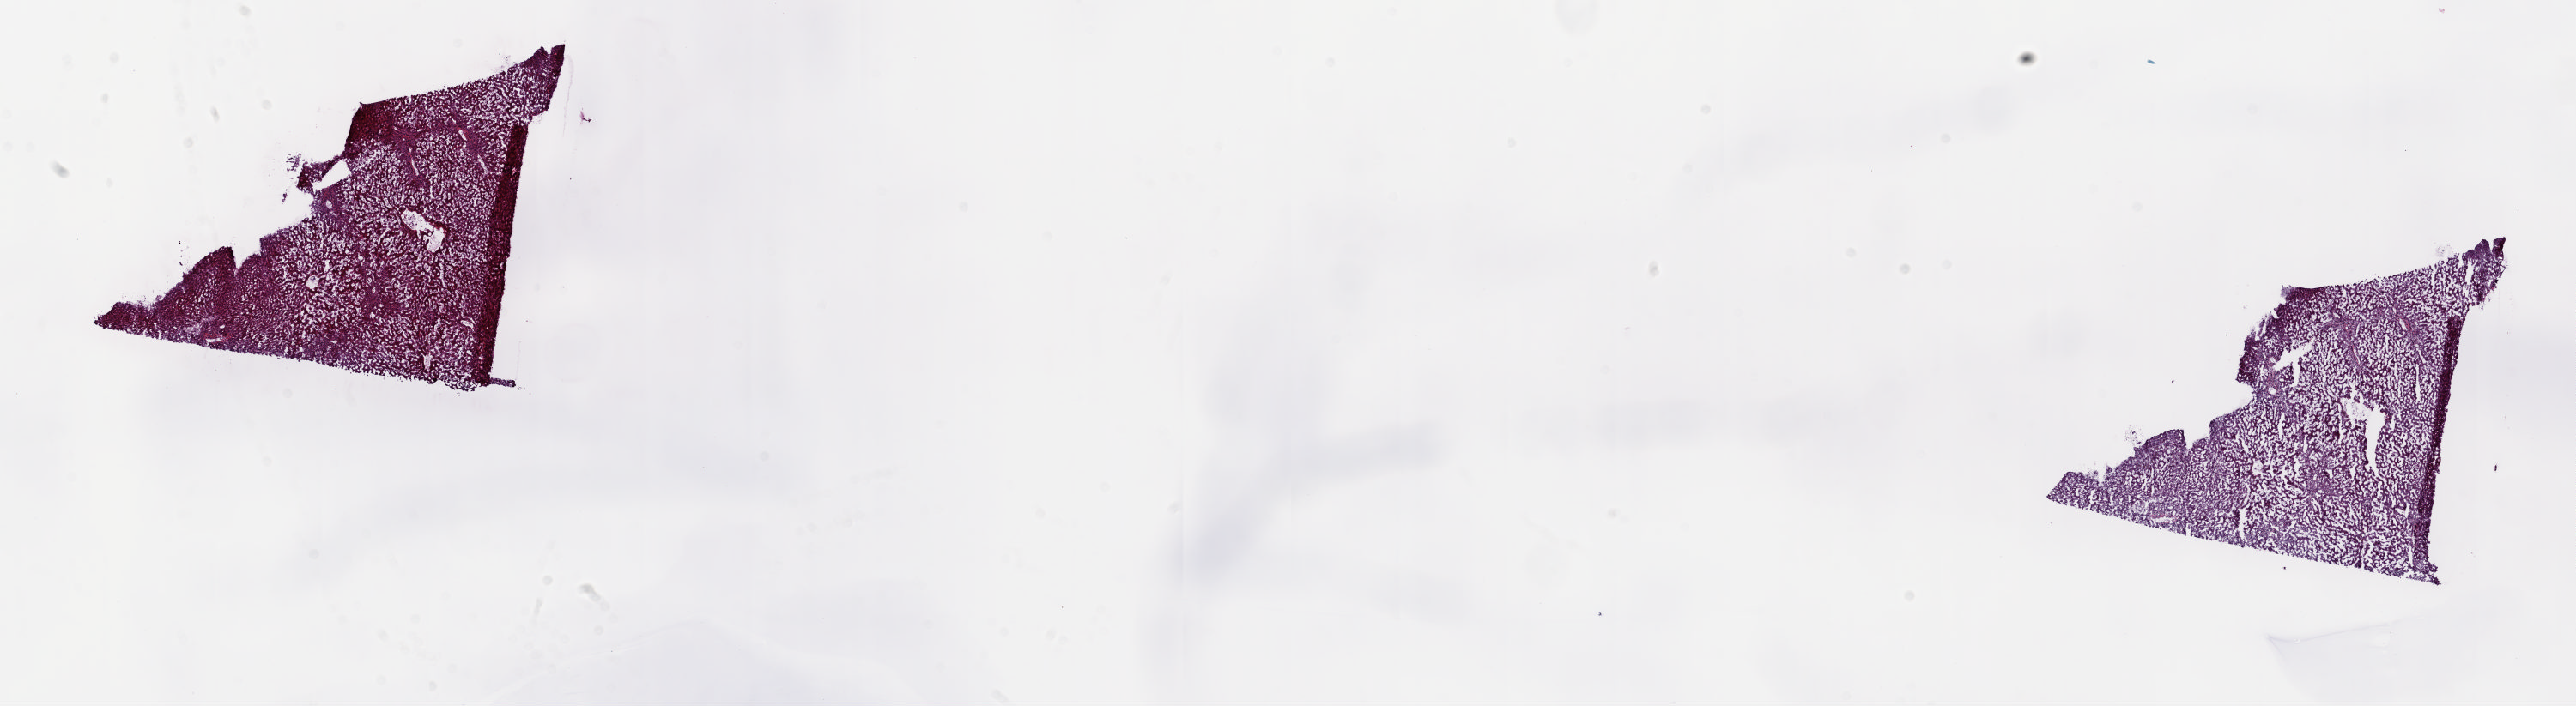
Digitized H&E-stained tissue section (whole slide), low-resolution overview of the scanned area, about 23.8 x 6.5 mm; frozen section from the top of the tissue portion; liver, solid tissue normal (non-tumour tissue) sample. Male patient; age at initial diagnosis 68 years. Slide review estimates, as recorded: tumour cells 0%, tumour nuclei 0%, normal cells 100%, stromal cells 0%, necrosis 0%. Inflammatory infiltration, as recorded: lymphocyte infiltration 0%, monocyte infiltration 0%, neutrophil infiltration 0%.
This section: solid tissue normal (non-tumour) sample from the same patient. Patient diagnosis: Hepatocellular carcinoma, NOS.